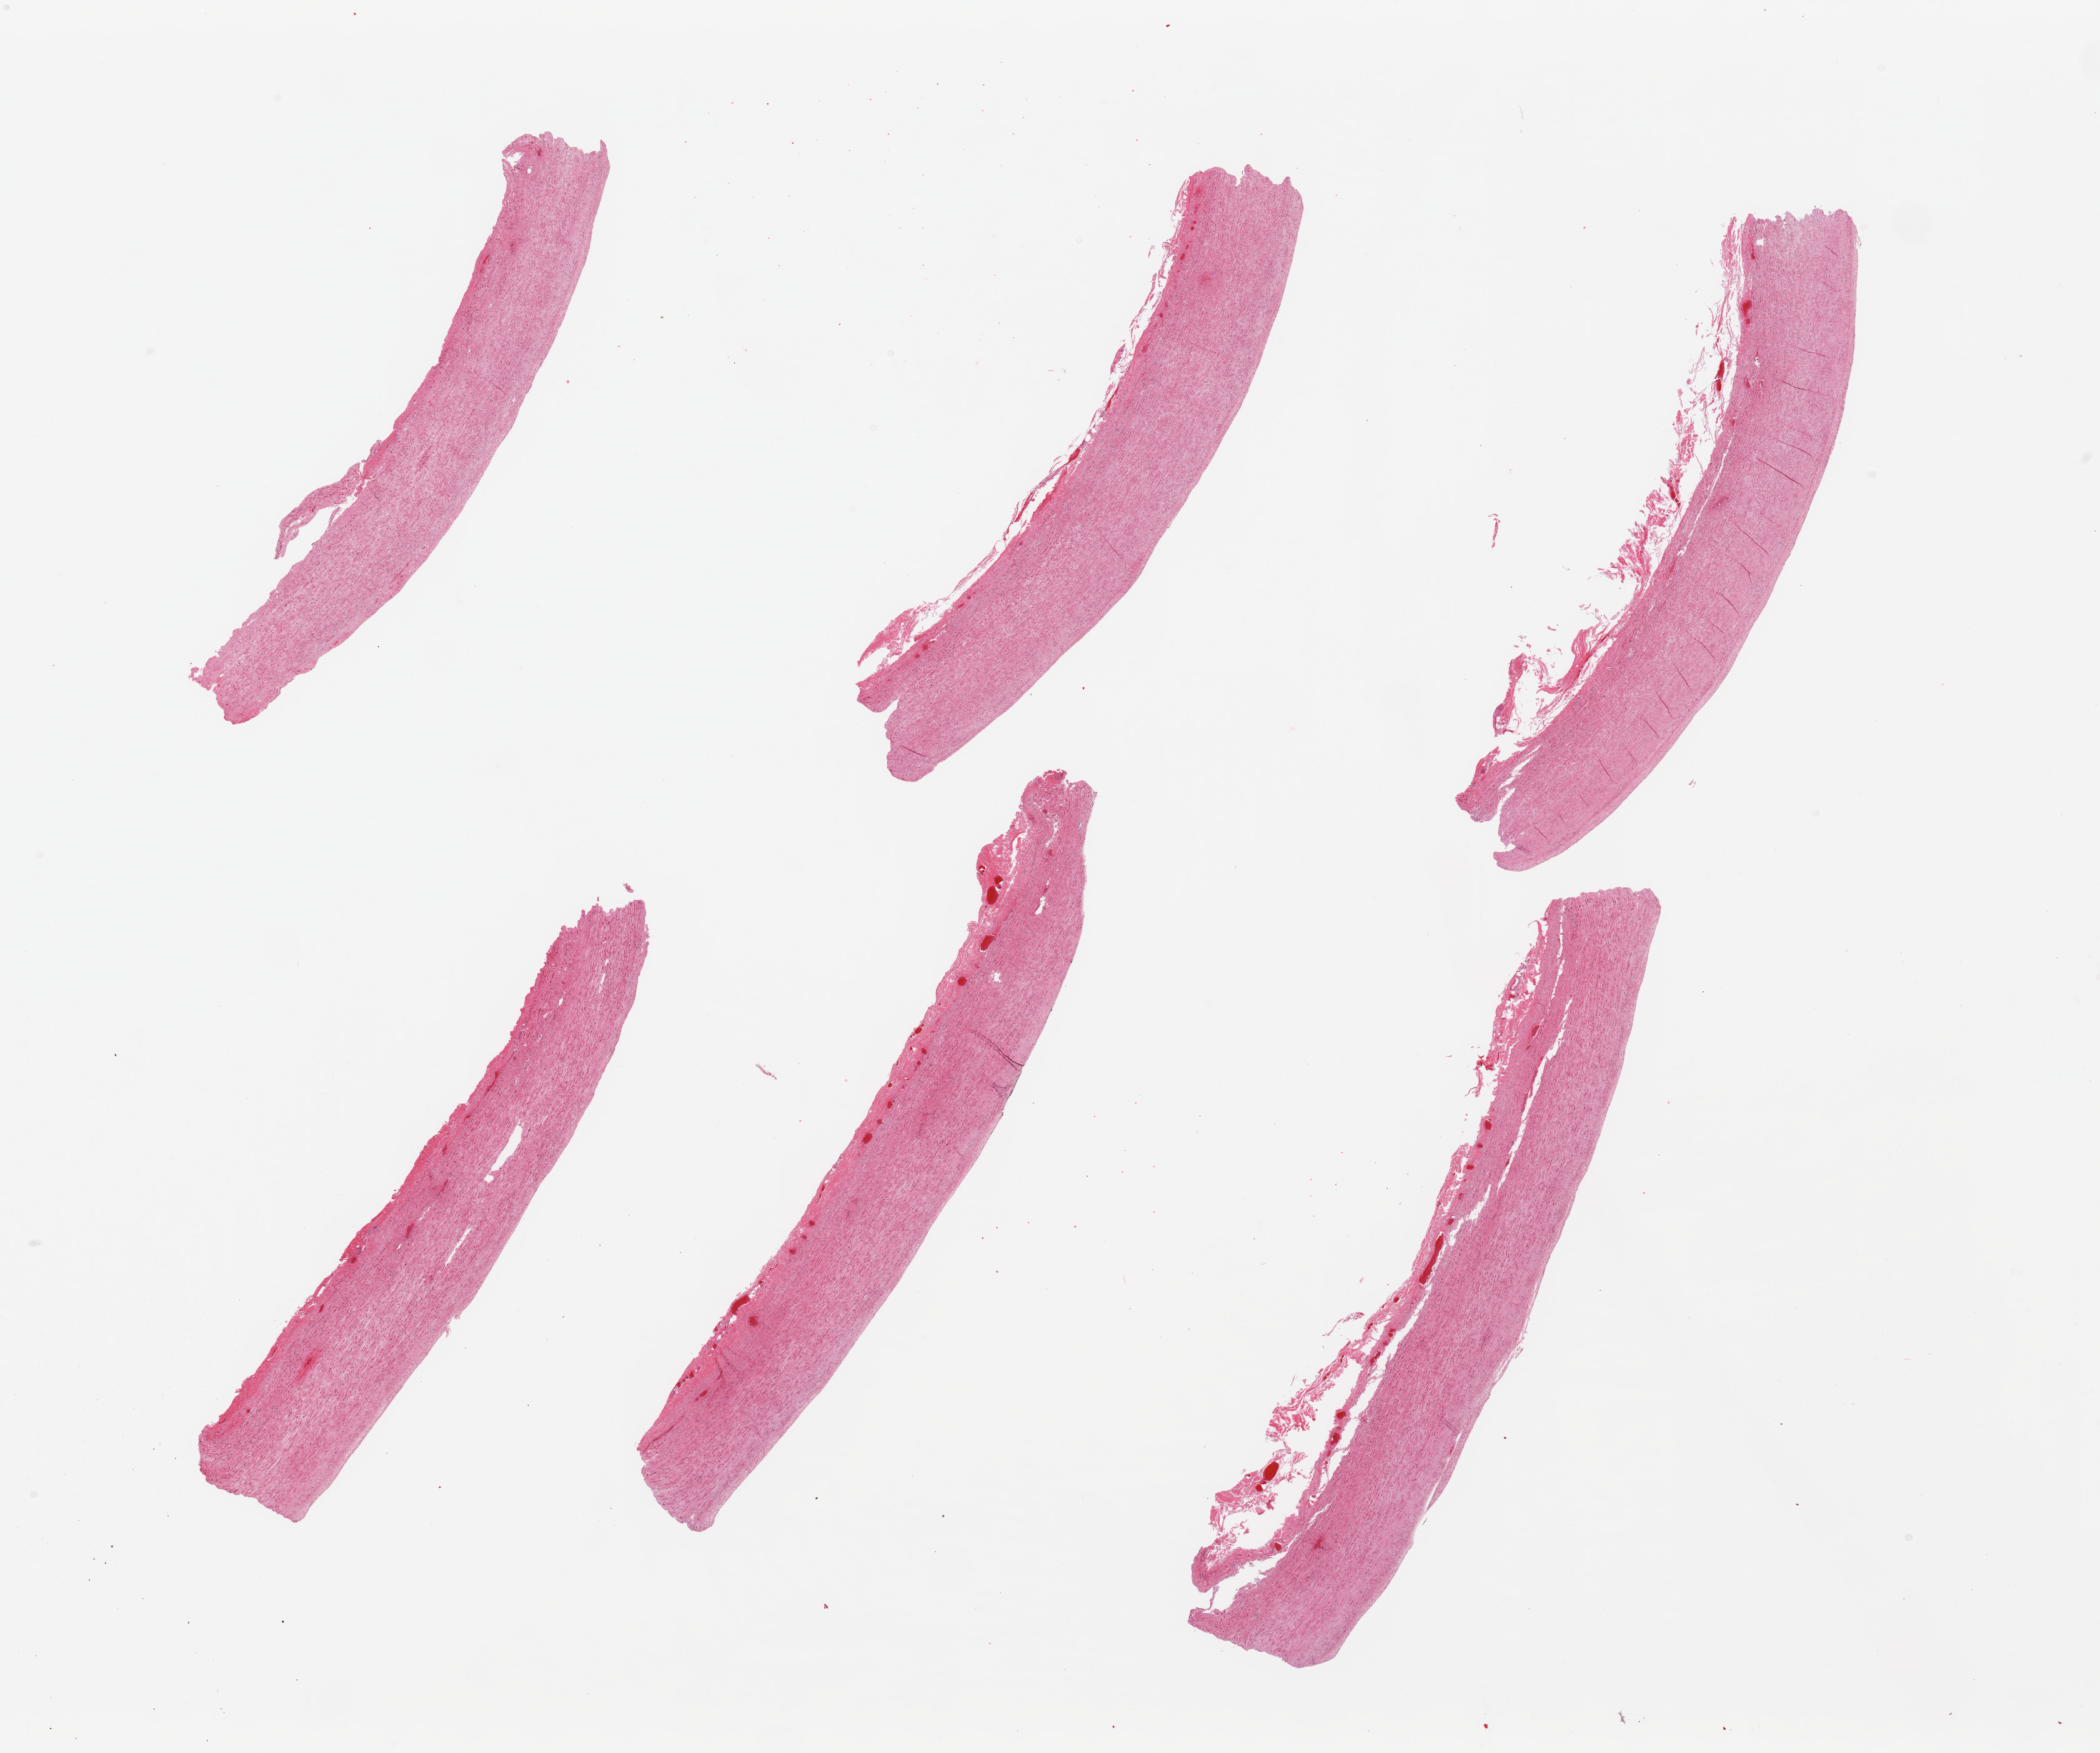
Whole-slide image, hematoxylin and eosin (H&E) stain — a low-resolution overview of the entire scanned area, about 26.6 x 22.2 mm (acquisition: 20x scan). PAXgene-fixed paraffin-embedded (PFPE) section. Target tissue: aorta. Tissue donor sample. Donor: male.
Pathologist's review note for this sample: 6 pieces, atherosis < 0.1mm.